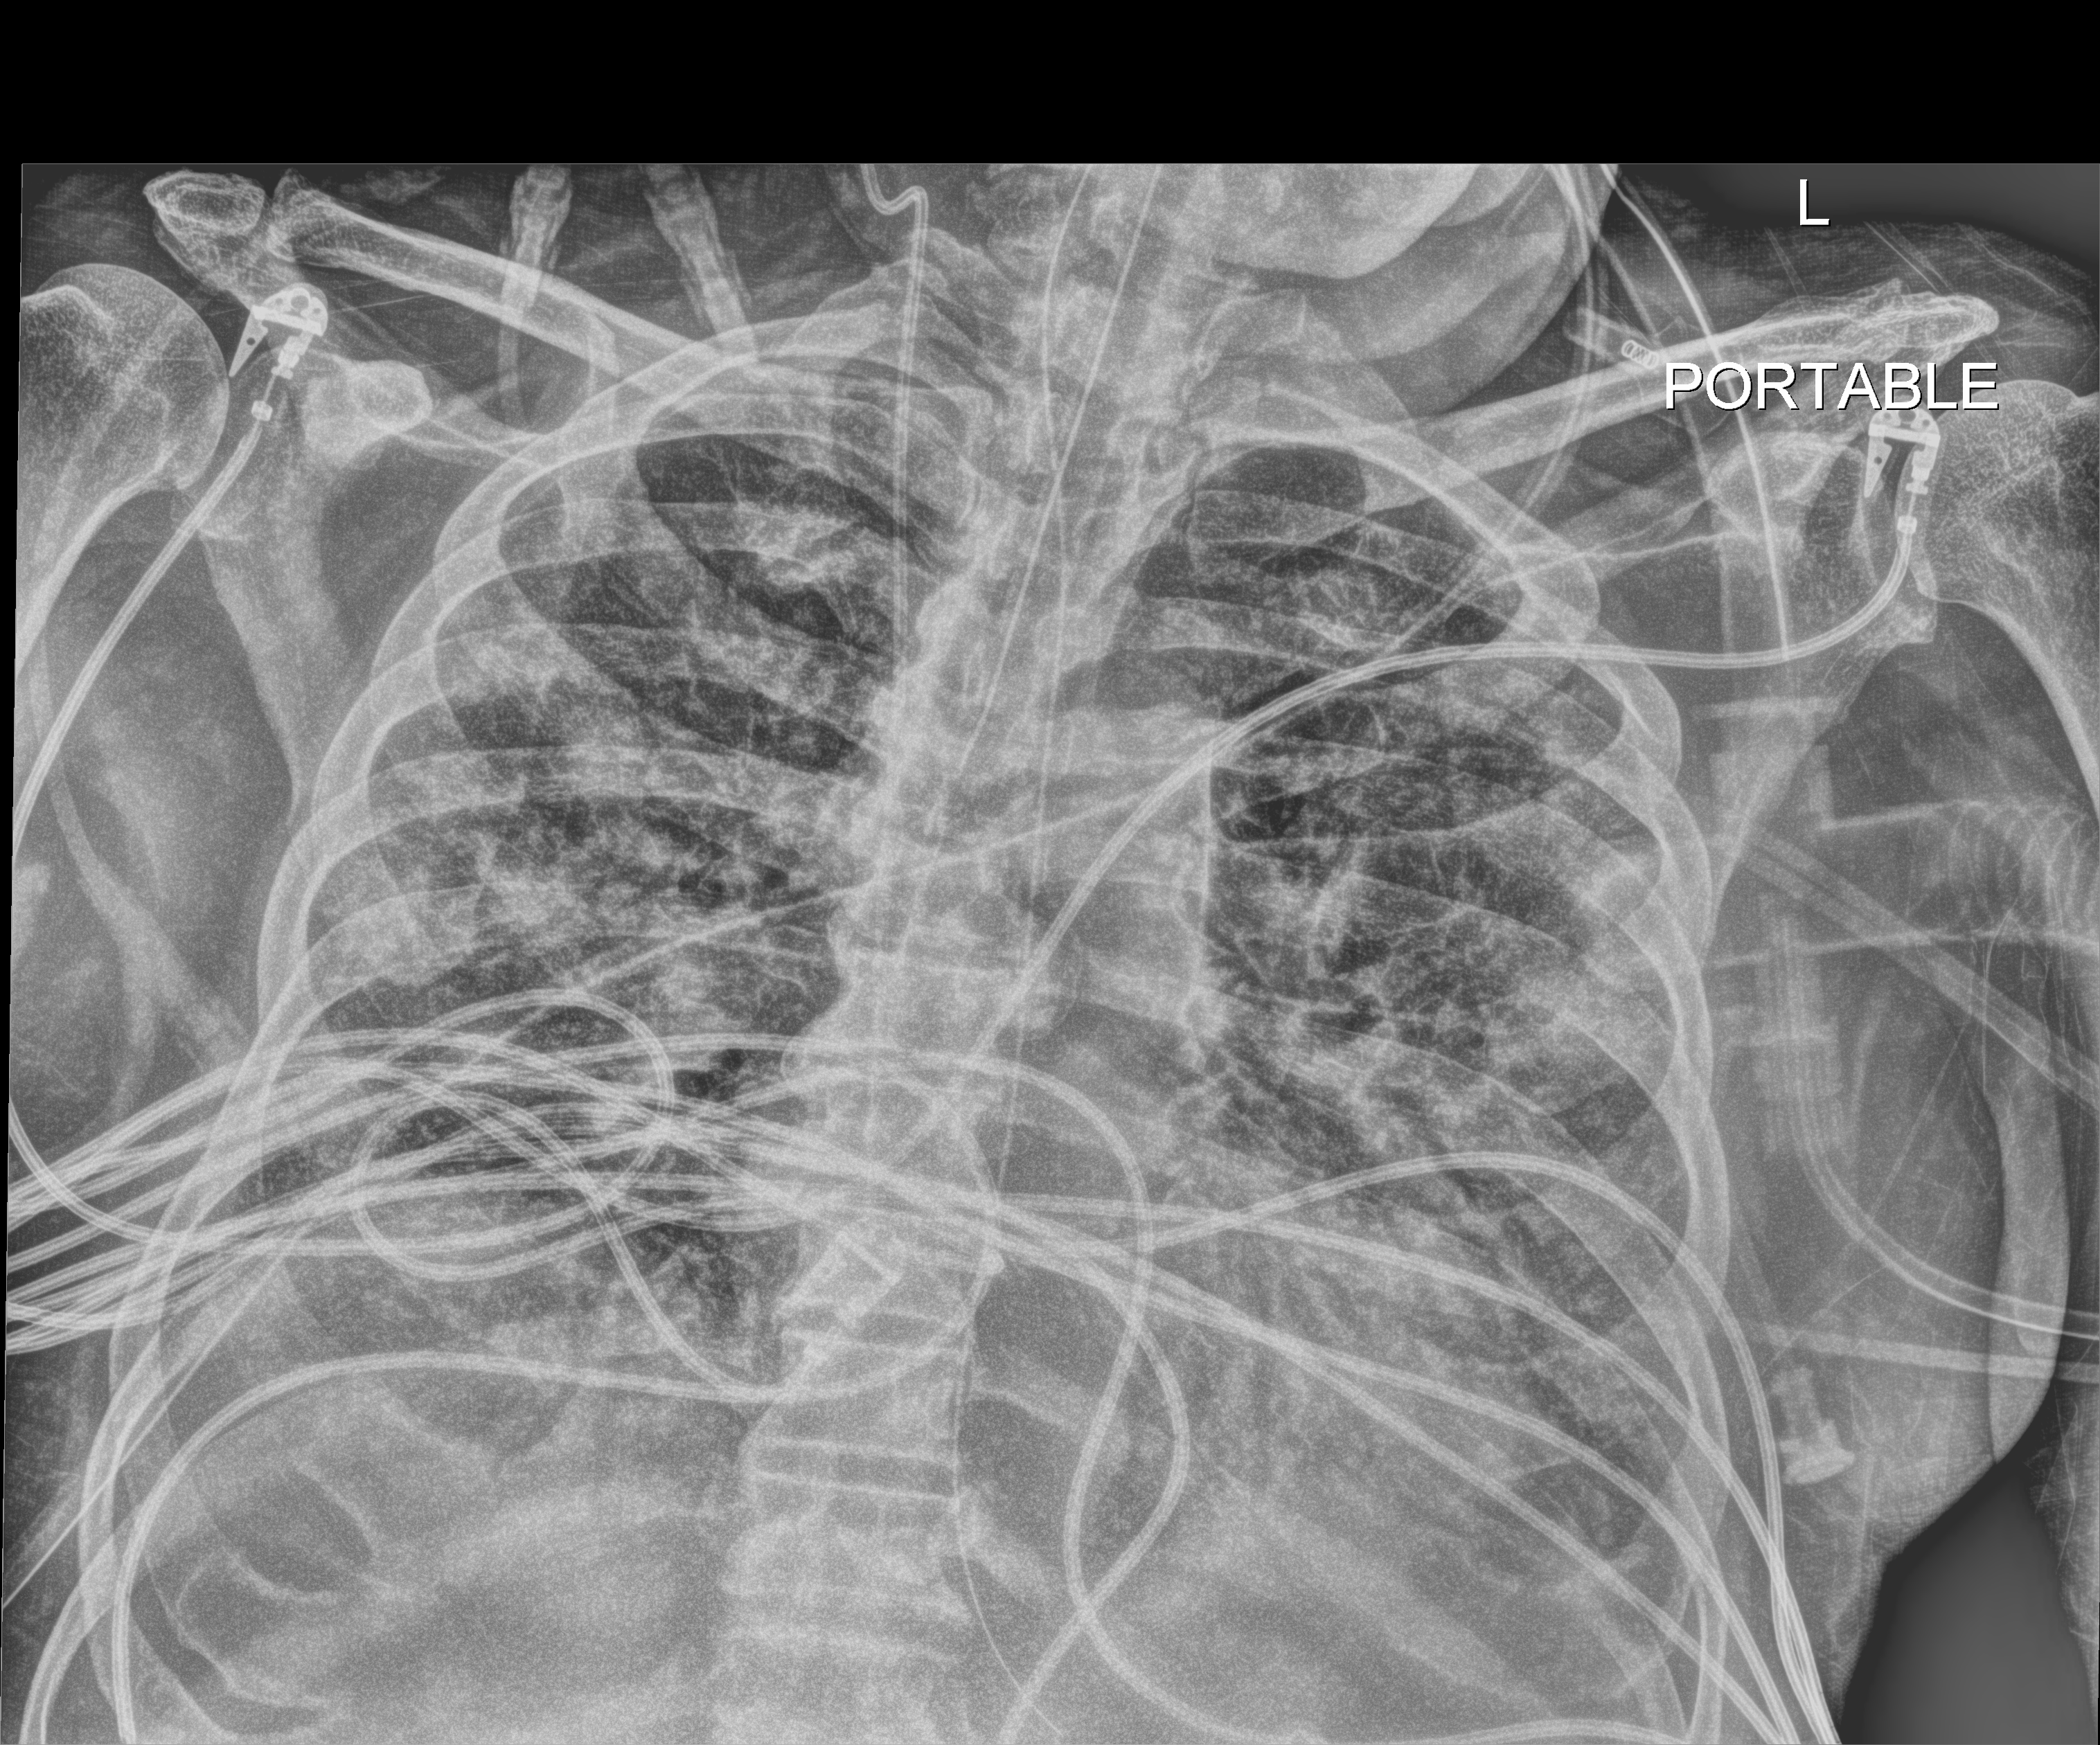
Bedside chest radiograph (digital radiography), anteroposterior (AP) projection. Male patient hospitalised with COVID-19, age 75–90 years.
Hospital-stay facts (about this admission, not read from this image; timing relative to this image not recorded): admitted to intensive care during this hospital stay: yes; other chronic lung disease (admission record): no; length of hospital stay: 33 days.